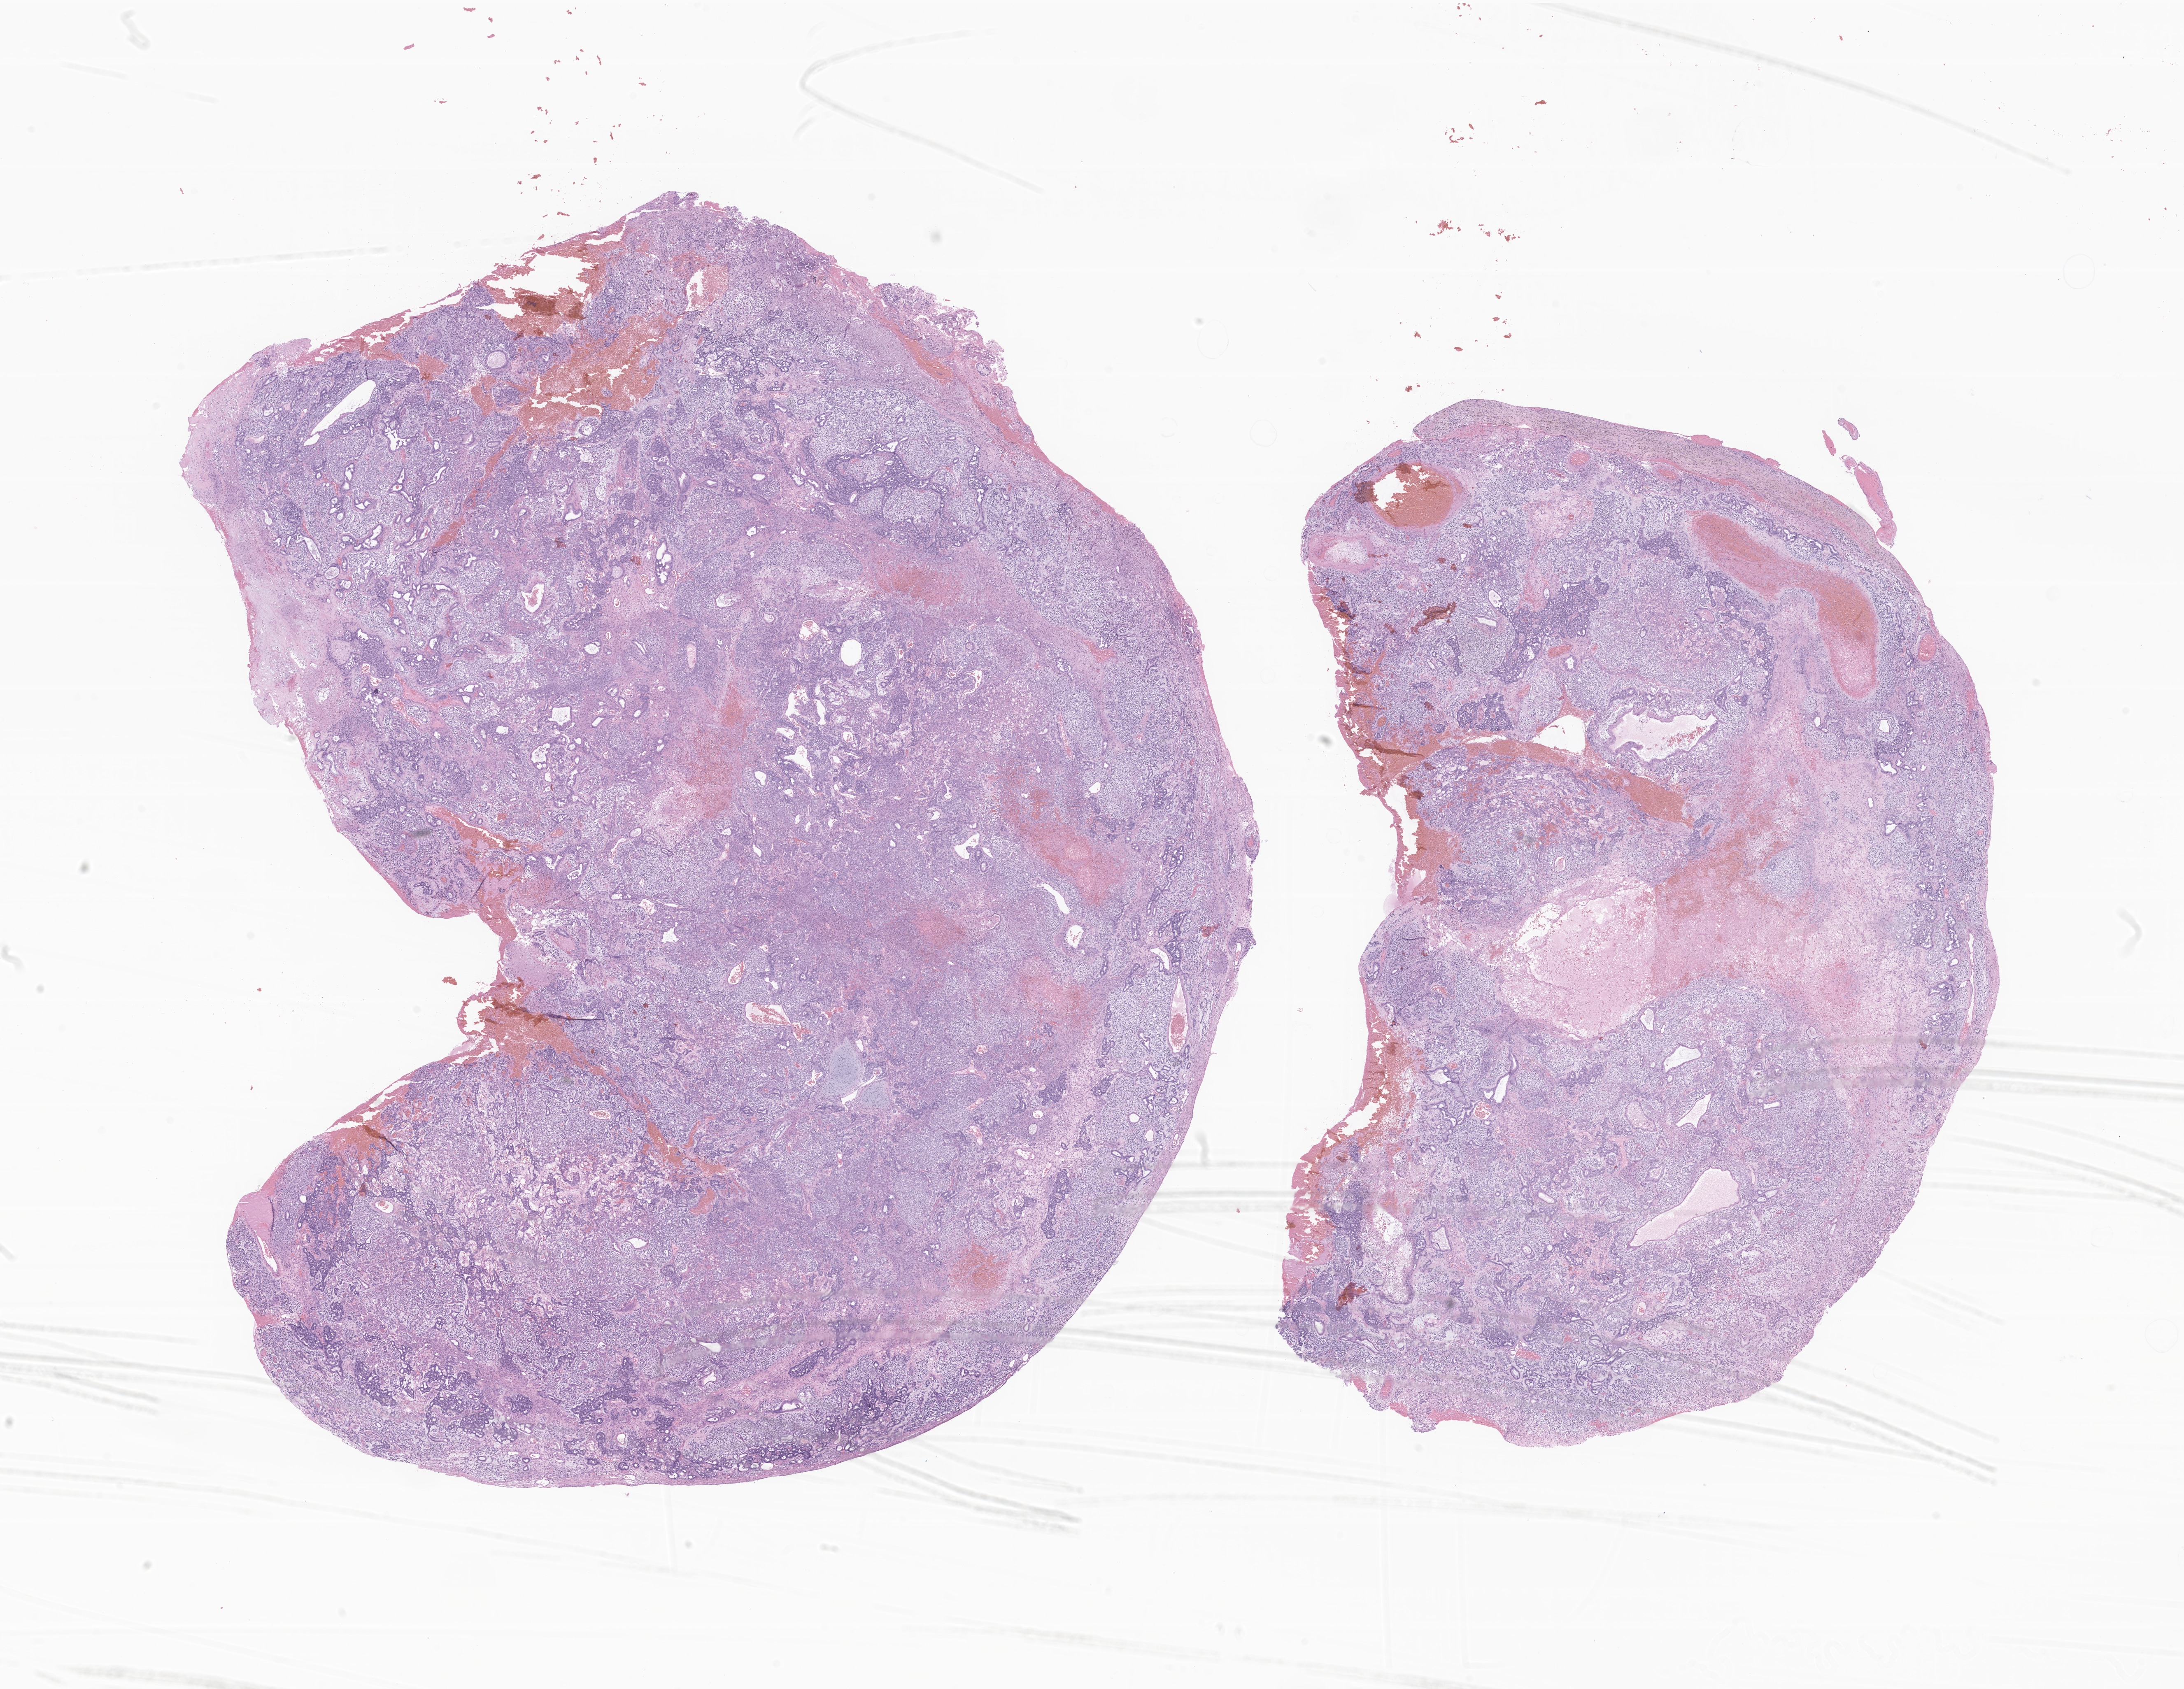
Hematoxylin and eosin (H&E) whole-slide image of tumor tissue from the cerebral ventricle, low-resolution overview of the scanned area, about 22.4 x 17.3 mm. Formalin-fixed, paraffin-embedded (FFPE) tissue. Patient: male, age 187 months (15 years 7 months).
• recorded diagnosis: Mixed germ cell tumor